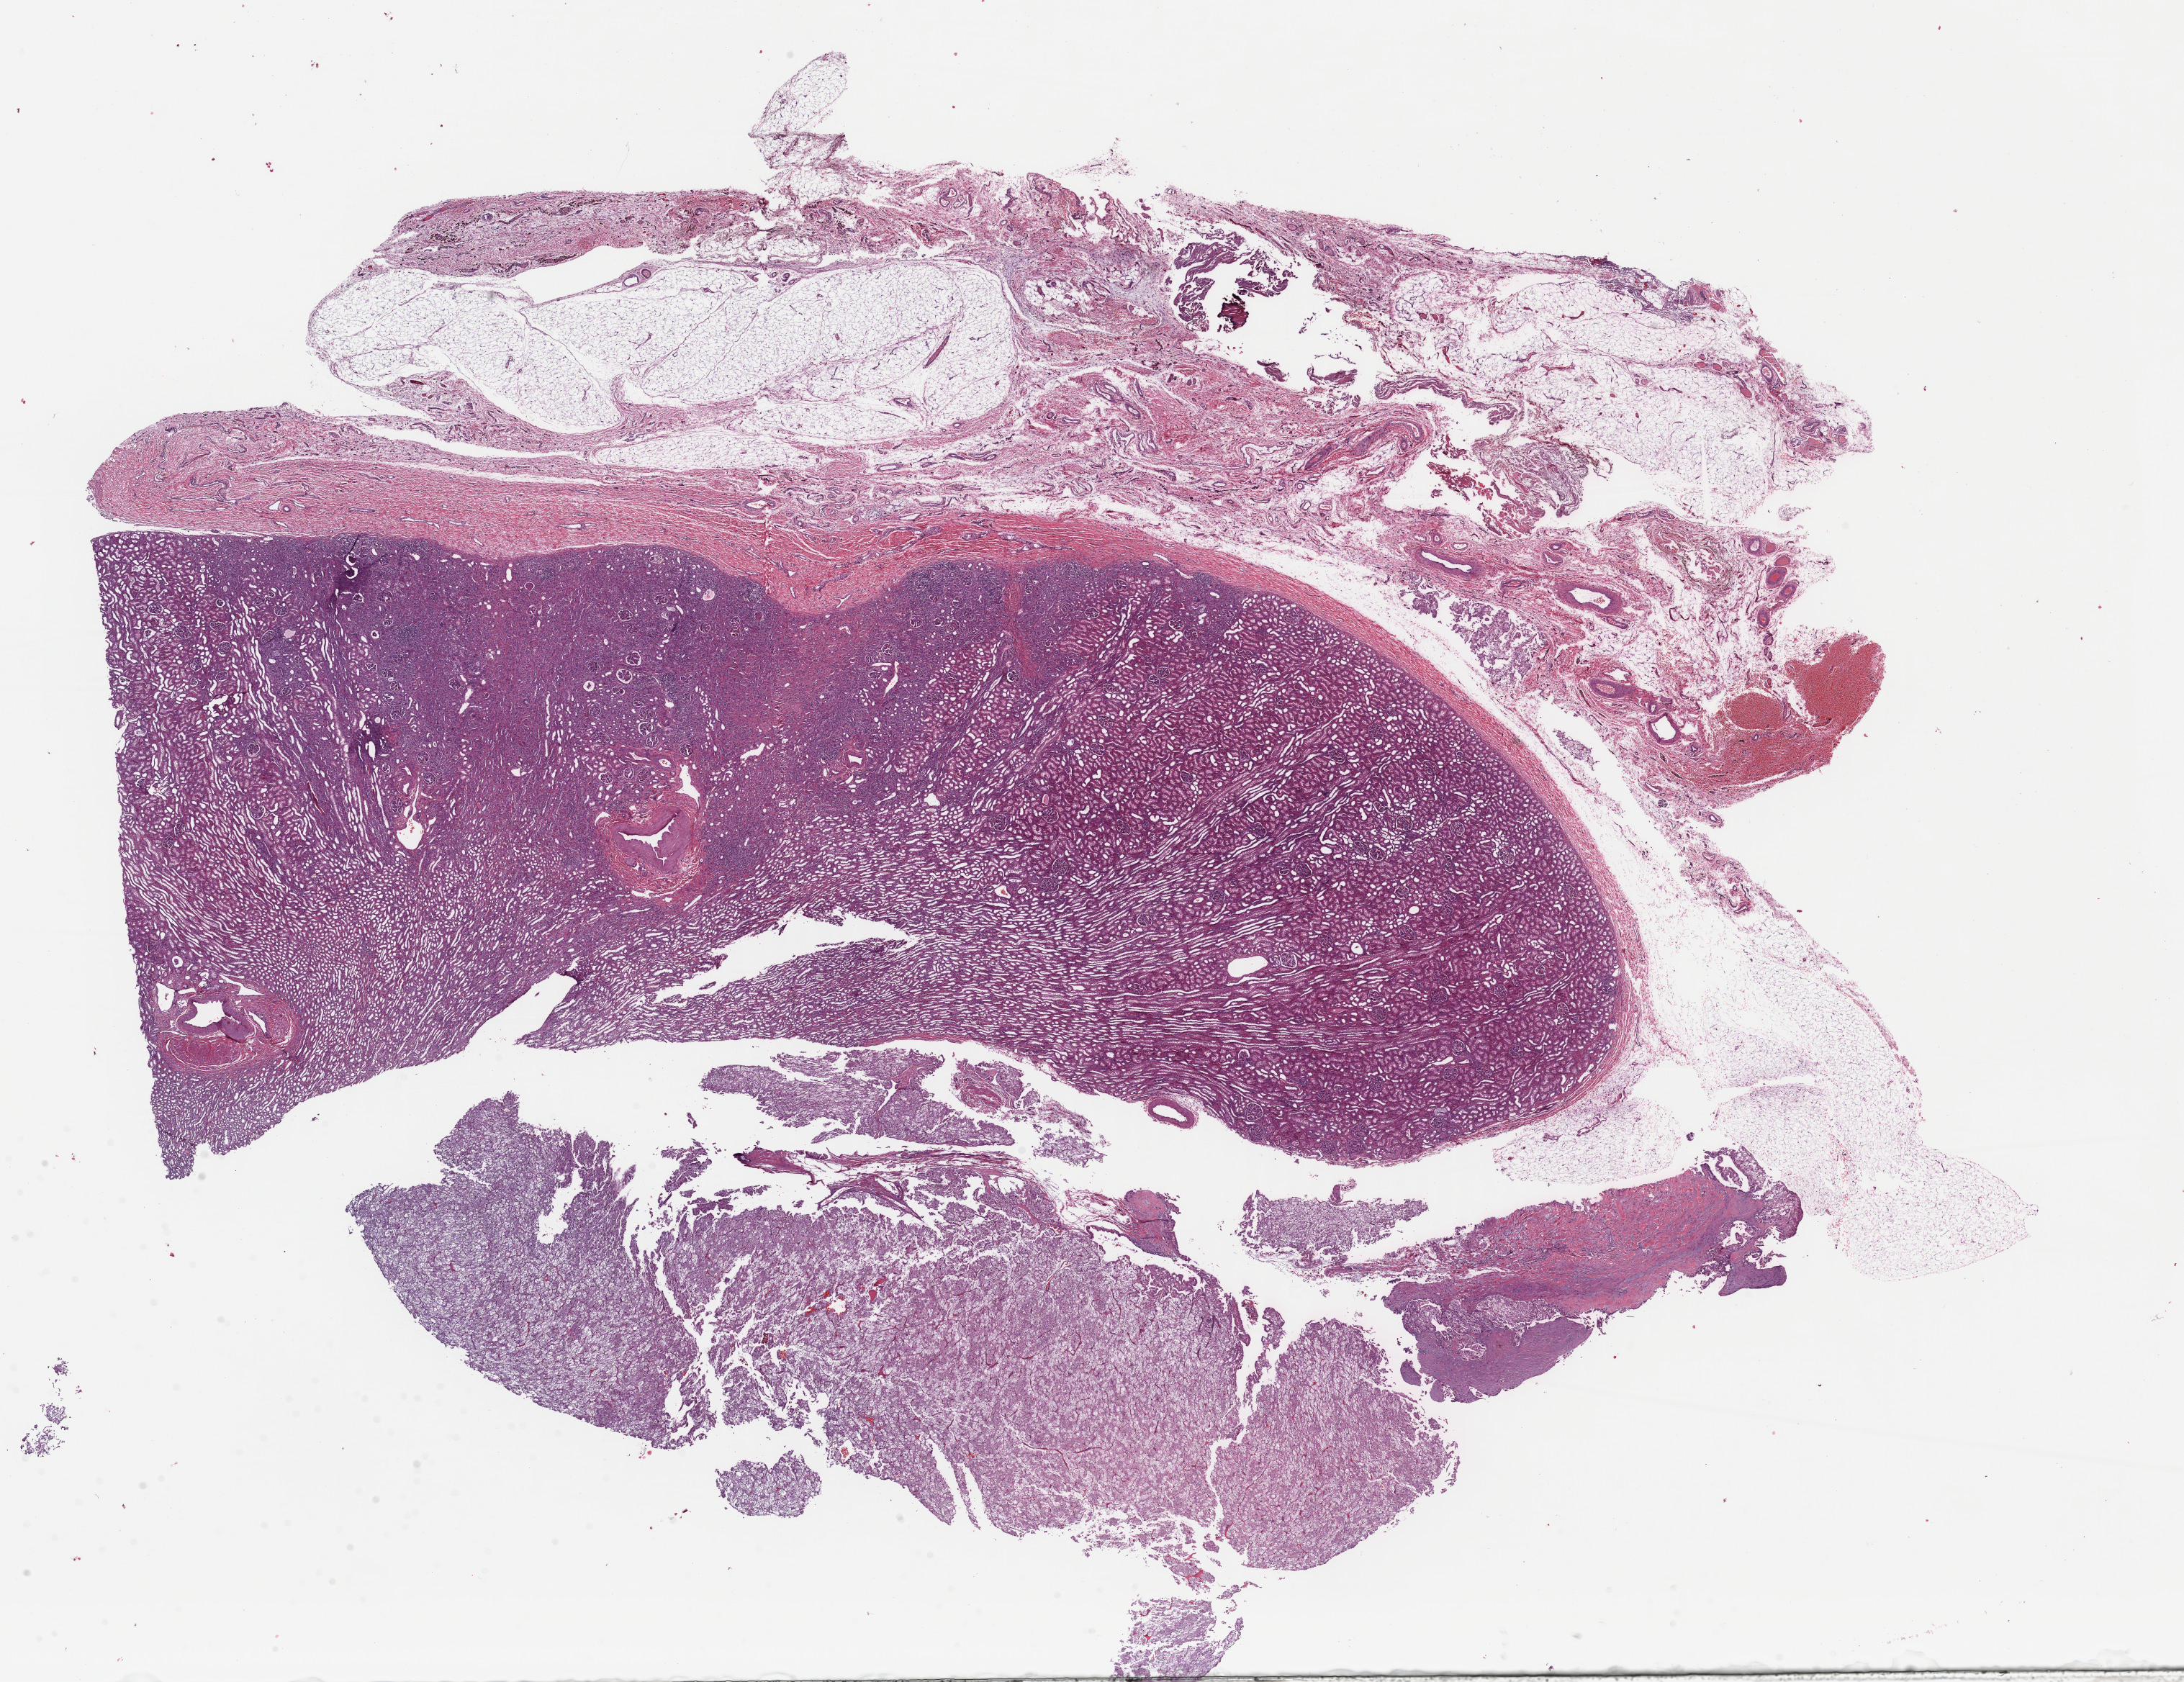
Hematoxylin and eosin (H&E) stained whole-slide image, a low-resolution overview of the entire scanned area, about 23.9 x 18.4 mm (slide scanned at 40x), formalin-fixed paraffin-embedded (FFPE) diagnostic section, sample: primary tumour, kidney. Patient: female, age at initial diagnosis 17 years.
• AJCC pathologic stage: I (7th edition)
• histologic diagnosis: Renal cell carcinoma, chromophobe type